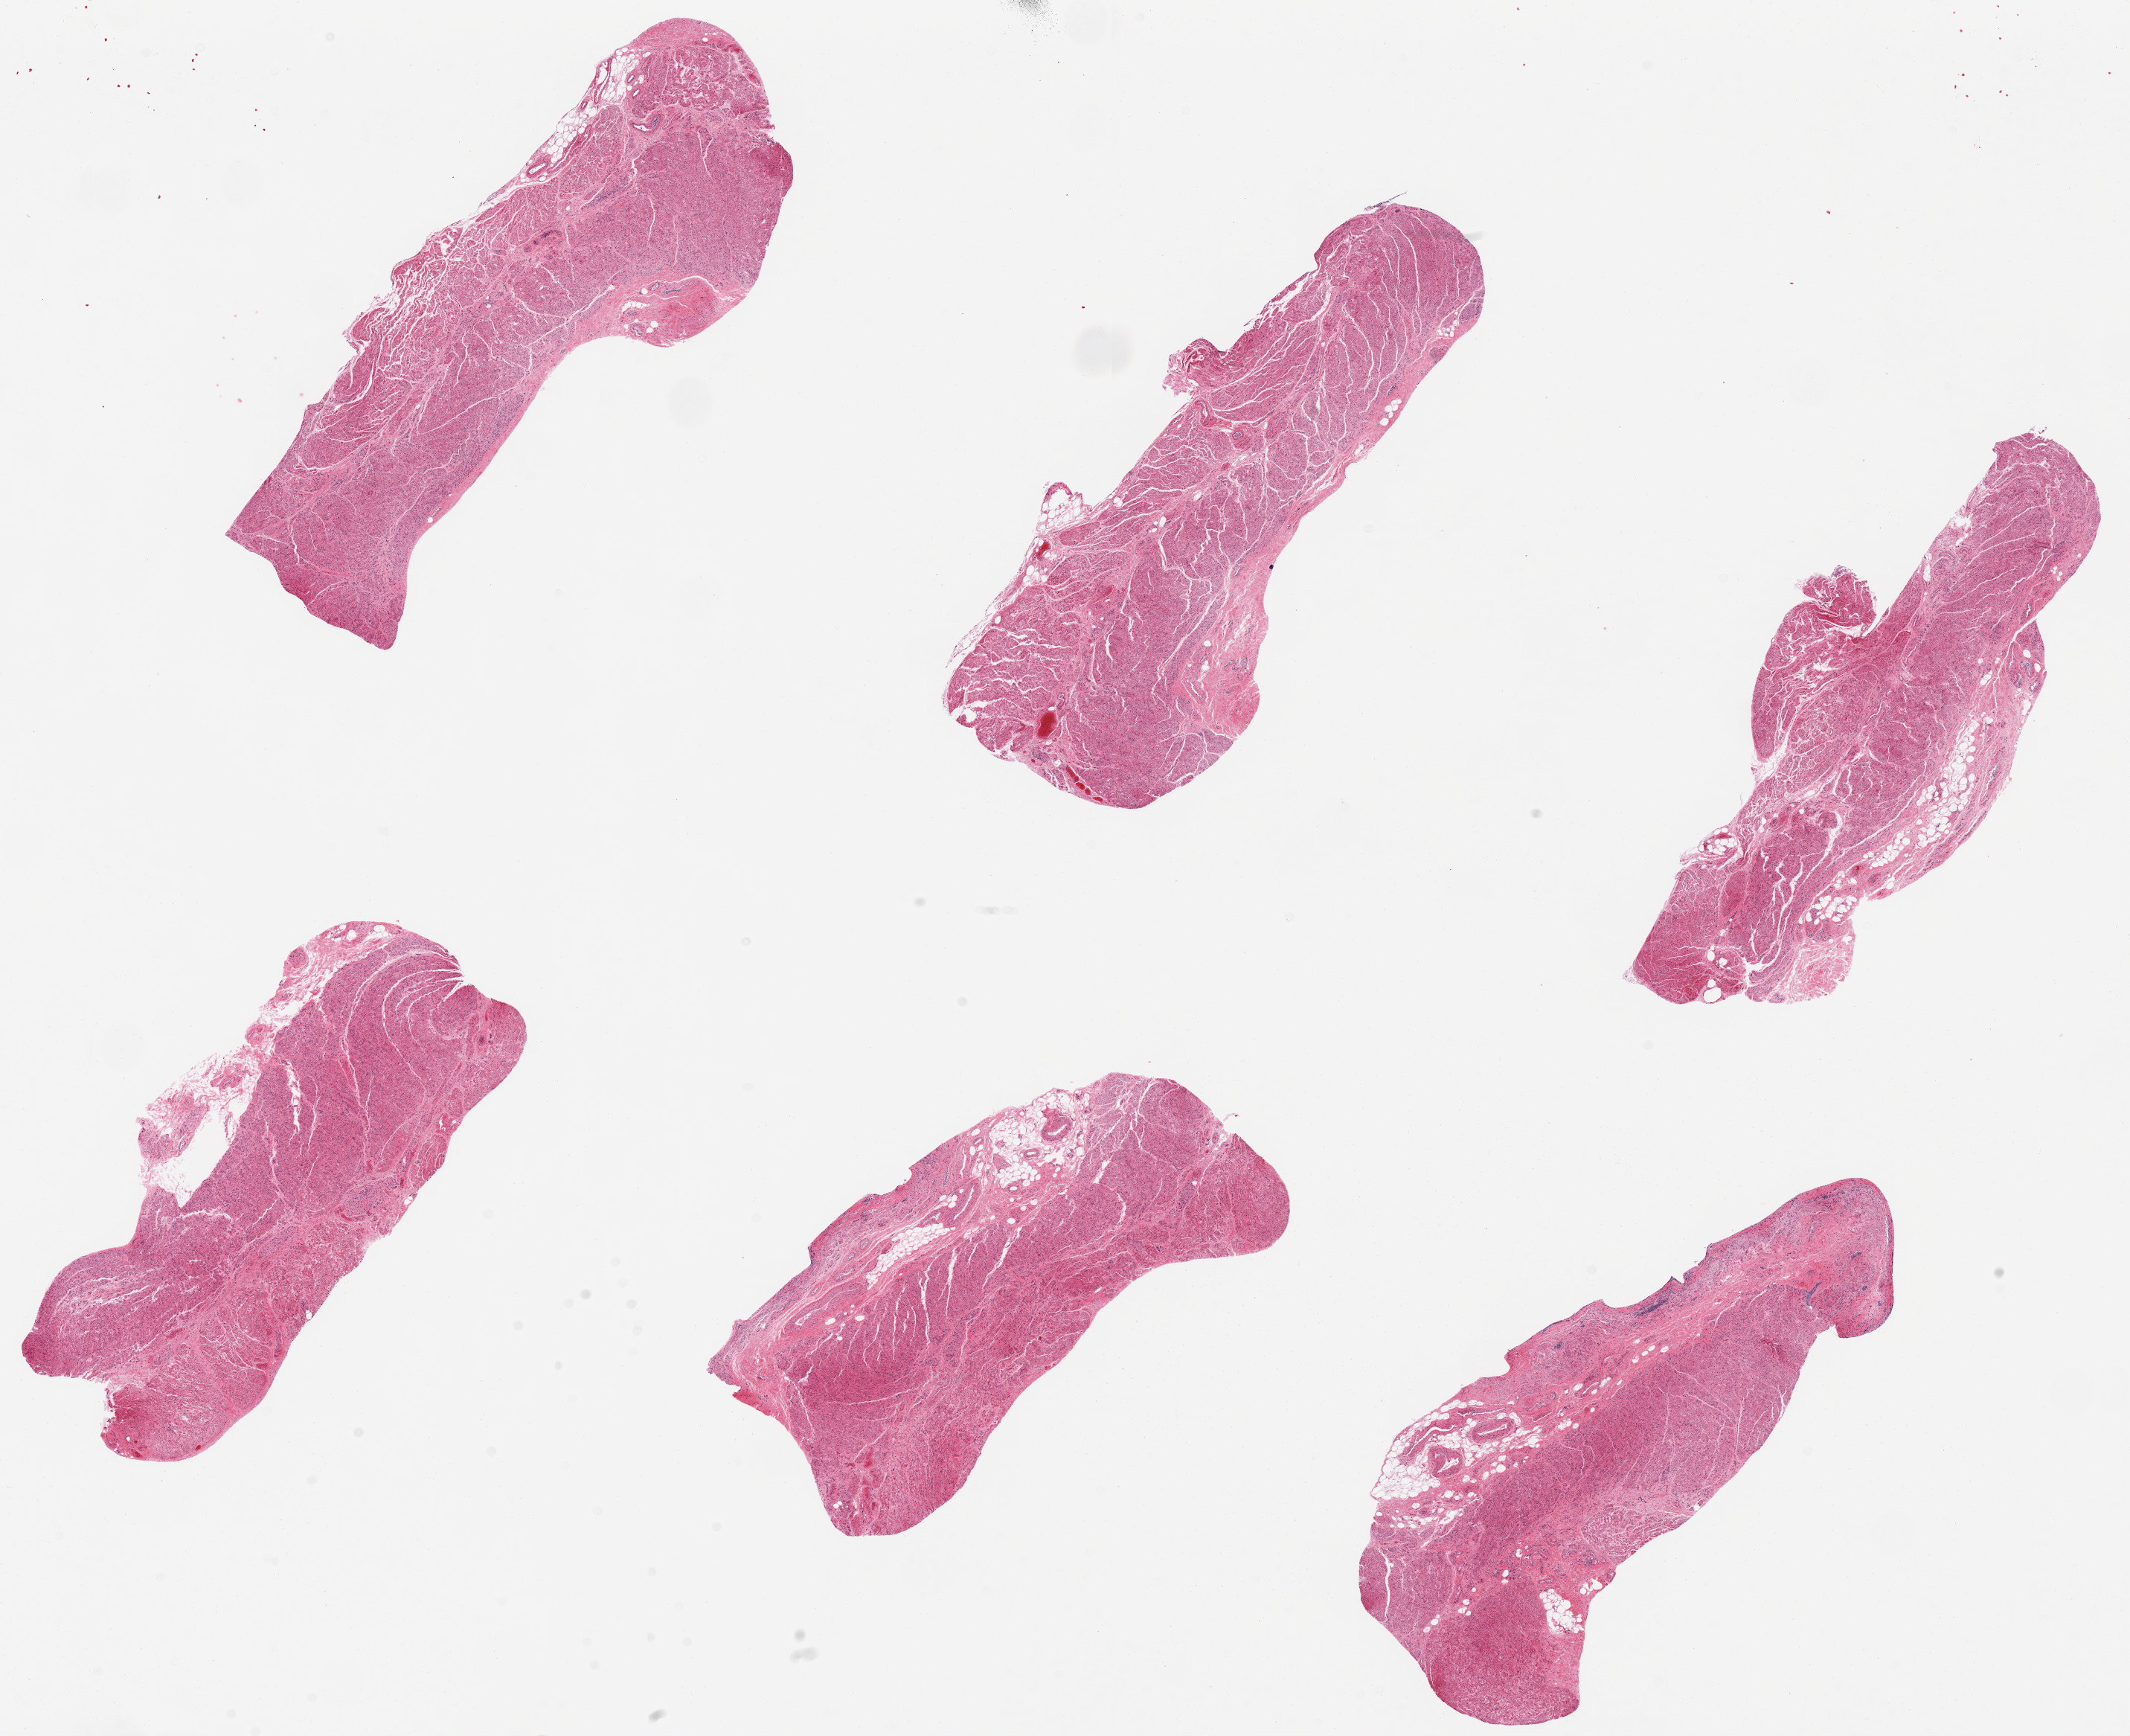
Whole-slide image, hematoxylin and eosin (H&E) stain — shown as a low-resolution overview of the whole scanned area (about 22.6 x 18.5 mm); PAXgene-fixed paraffin-embedded (PFPE) section; section of gastroesophageal junction (target tissue); donor tissue sample.
Reviewer comment on this tissue sample: 6 pieces.